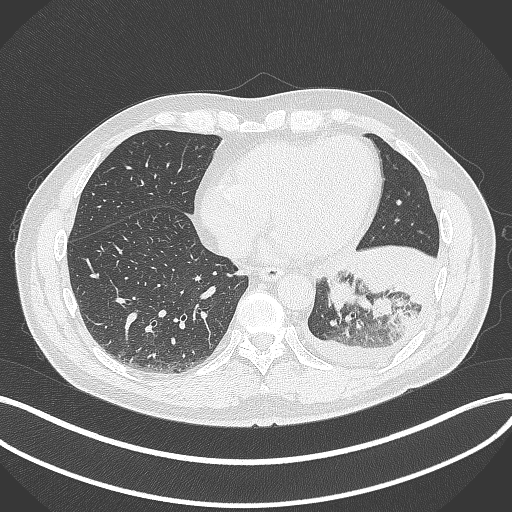
Chest CT, one axial slice. Position 111 of 342 along the scan axis. Reconstruction kernel B70f. 120 kVp. Lung window (W 1500 / L -600 HU). 512 × 512 image matrix. Male patient, age 58 years. From the clinical record (not read from this slice): clinical TNM (as recorded): T3 N1 M1b; histopathological grade: G3.
Outlined on this slice (rectangle marked by the reading radiologist):
- lung tumour (recorded histology: small cell carcinoma): bounding box (x1, y1, x2, y2) in pixels: (322, 270, 365, 311)